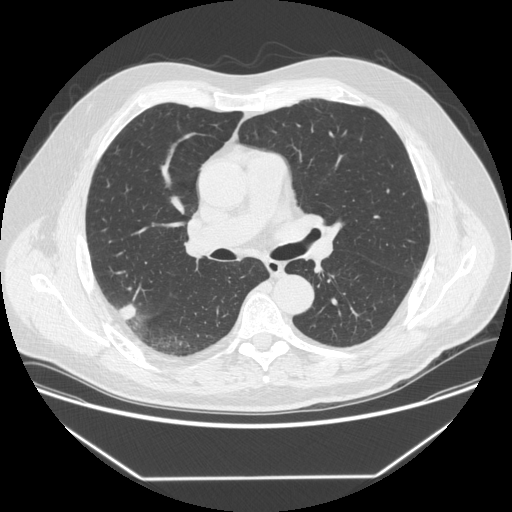
Axial slice from a low-dose chest CT screening exam, first (baseline) screen, lung window (W 1500 / L -600 HU), 1.25 mm slice thickness, slice 211 of 342 in the series, 512 × 512 image matrix, field of view 410 × 410 mm. Male, age 64 years at enrolment.
Expert reader's lesion annotation, box from (x=101, y=299) to (x=143, y=331) px. Reader record for this screening exam (exam-level; its link to the box is not recorded): non-calcified nodule or mass ≥4 mm, right upper lobe, 12 × 12 mm, smooth margins, soft tissue attenuation. Later outcome: lung cancer diagnosed 92 days after this screen — adenocarcinoma, NOS, right upper lobe, poorly differentiated (G3), stage IIIB (AJCC 6th edition), 15 mm at pathology.